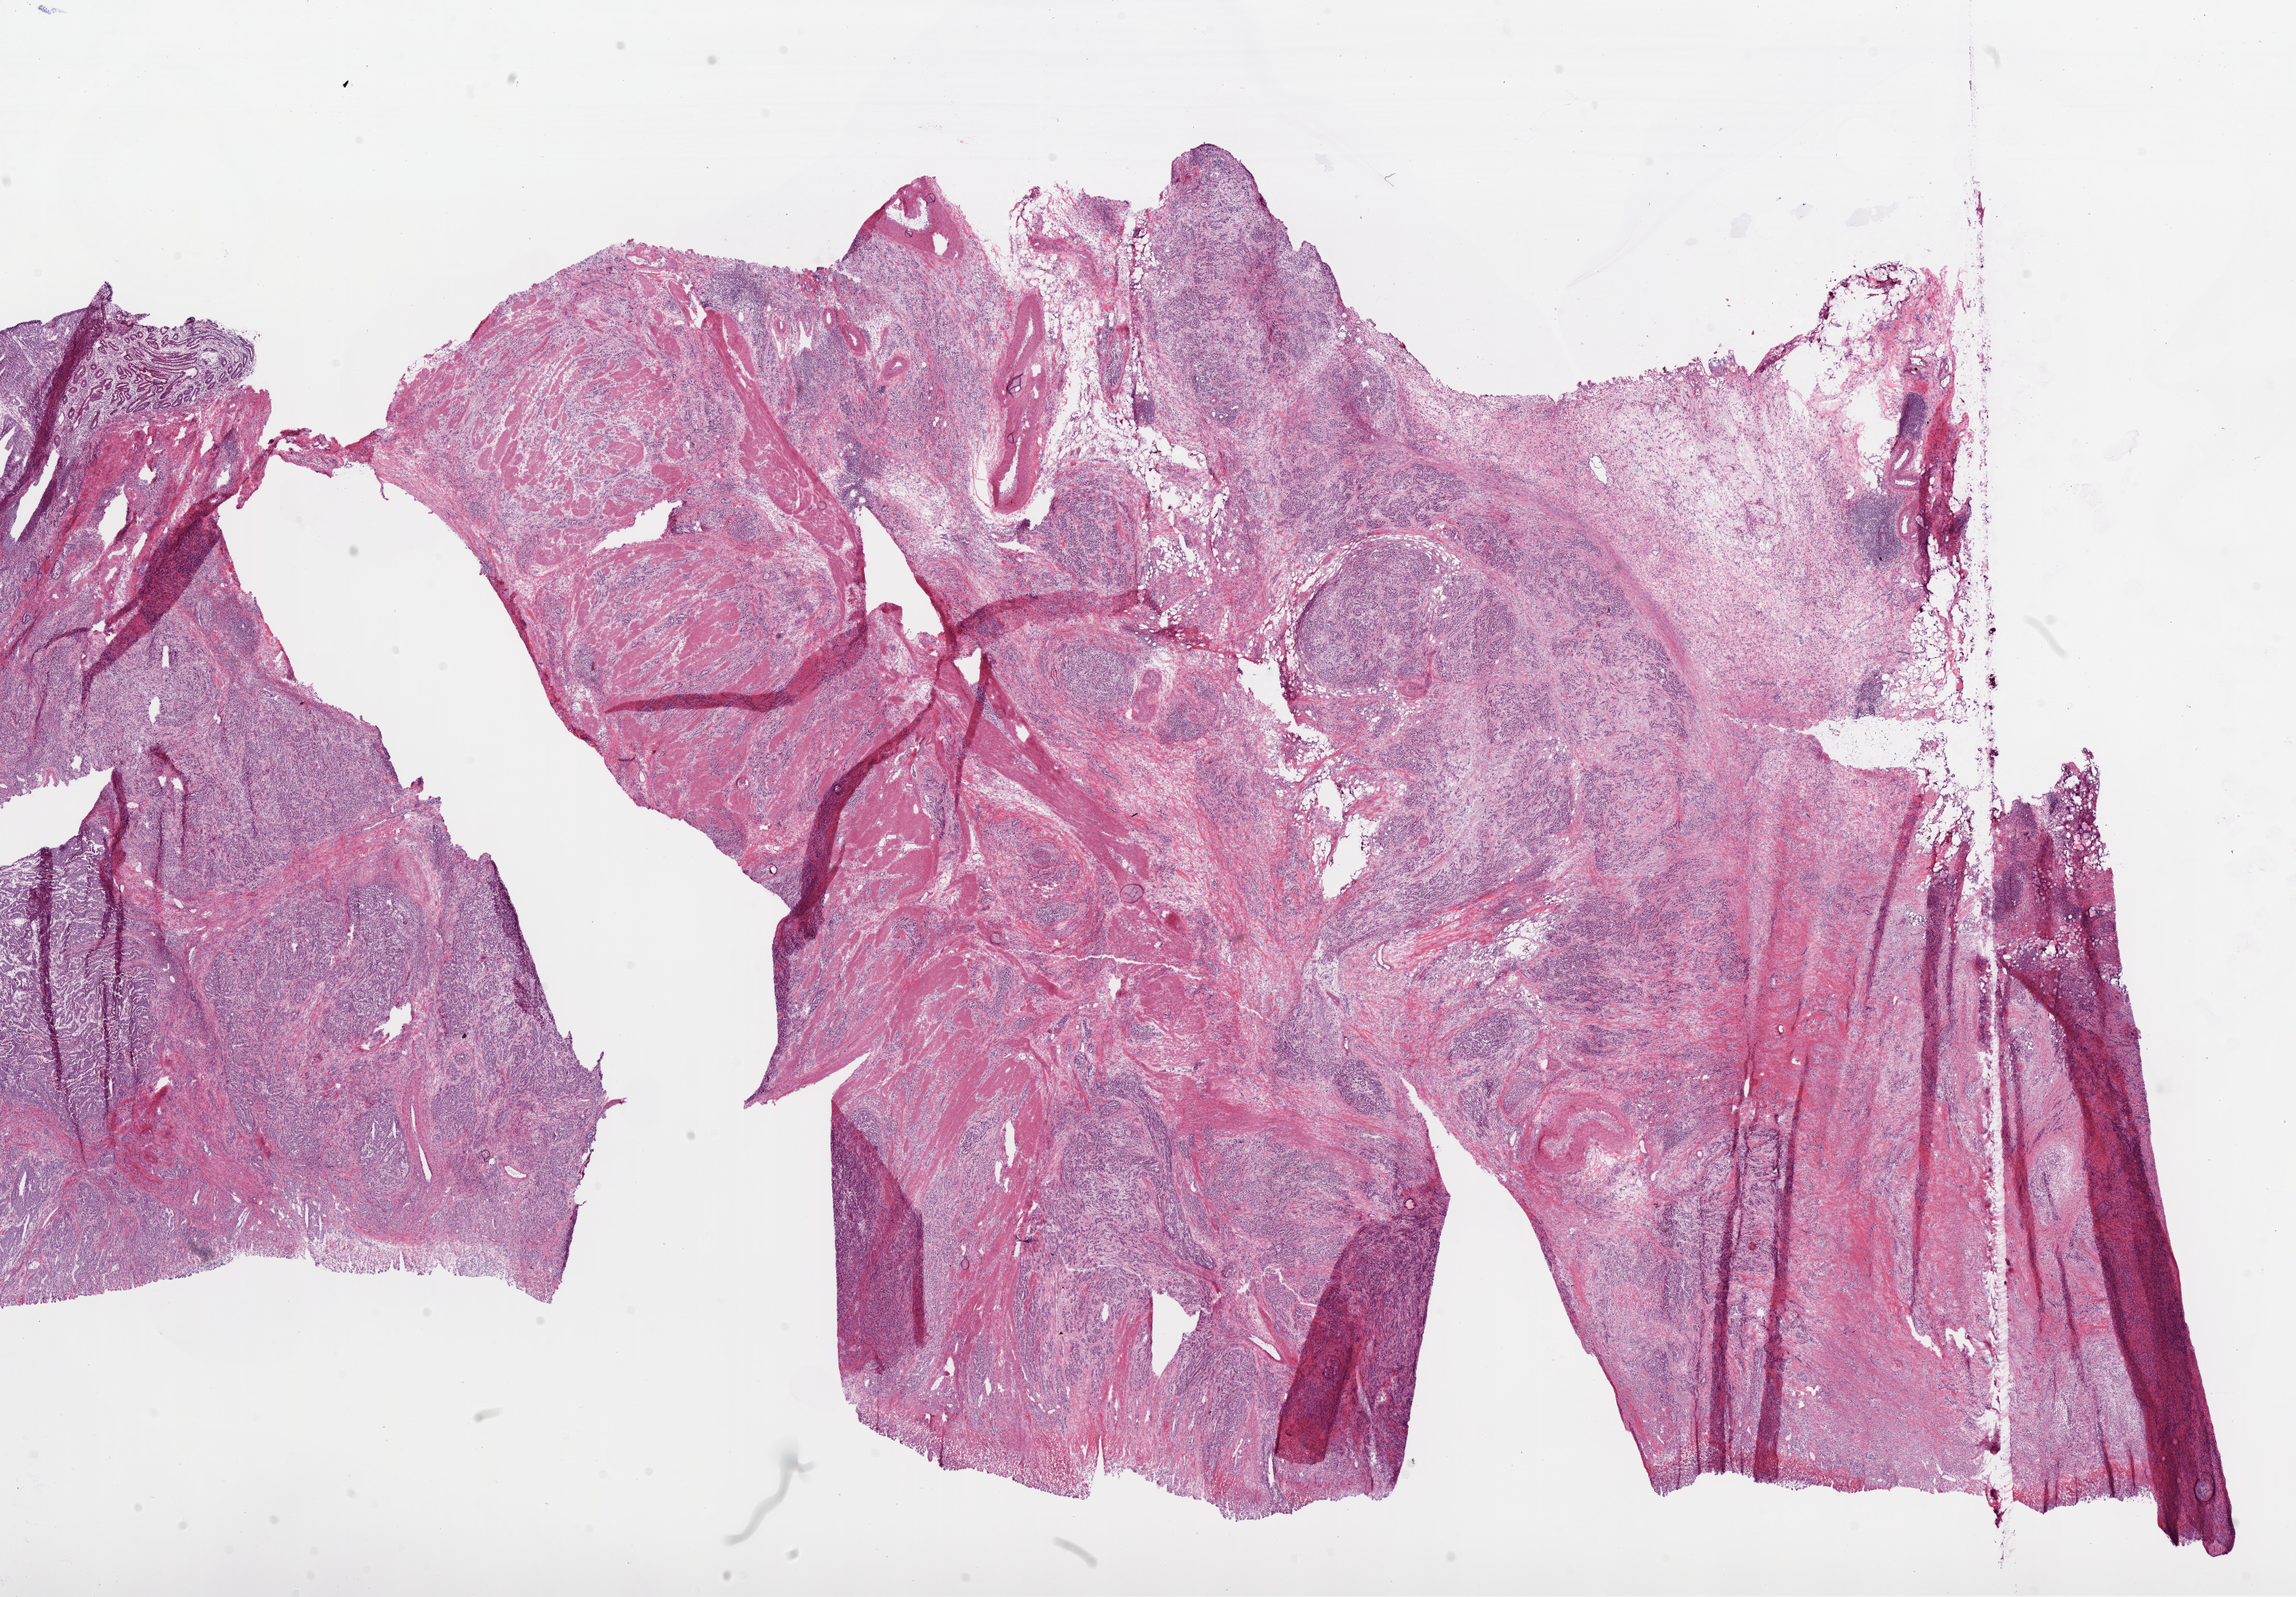
H&E whole-slide image — low-resolution overview of the scanned area, about 23.1 x 16.0 mm. Frozen section. Primary tumour sample from the stomach. Patient: female, age at initial diagnosis 55 years. Composition of this section per pathologist review: tumour cells 60%, tumour nuclei 65%.
Pathologic diagnosis: Adenocarcinoma, NOS (cardia, NOS).